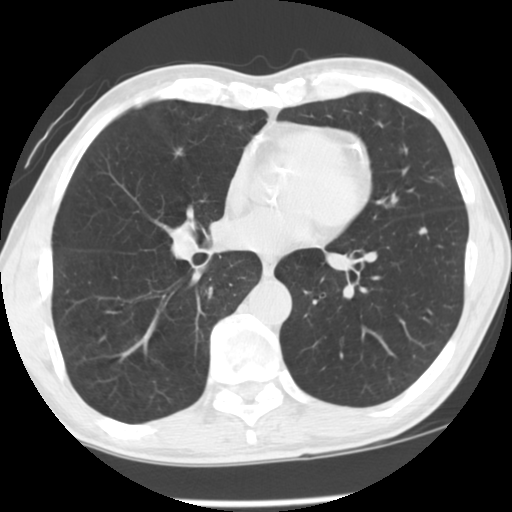
Chest CT (low-dose screening protocol), one axial image, third annual screen, lung window (W 1500 / L -600 HU), 2.5 mm slice thickness, 120 kVp, slice 78 of 139 in the series. Male participant, aged 63 years at enrolment.
- Expert-annotated lung lesion, bounding box <405,219,438,246> (left, top, right, bottom; pixels).
- Reader record for this screening exam (exam-level; its link to the box is not recorded): non-calcified nodule or mass ≥4 mm, left lower lobe, 6 × 5 mm, smooth margins, soft tissue attenuation, pre-existing on the prior screen: no.
- Official screen result: positive, other.
- Lung cancer was diagnosed 269 days after this screen: squamous cell carcinoma, NOS, left lower lobe, poorly differentiated (G3), stage IA (AJCC 6th edition), 4 mm at pathology.